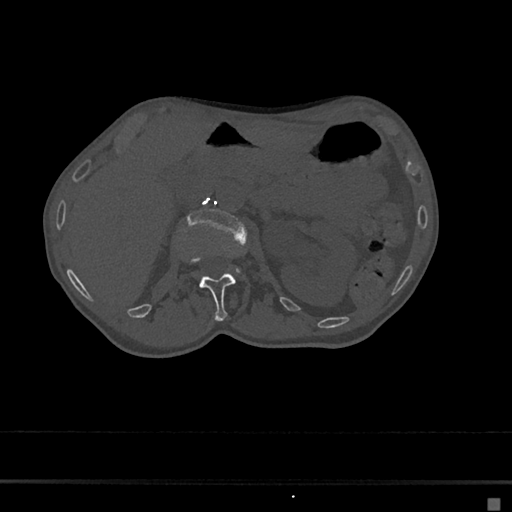
CT including the spine, one axial slice; slice 56 of 797 in the series (ordered by position); 120 kVp; bone window (W 1800 / L 400 HU); 0.5 mm slice thickness; 512 × 512 image matrix, field of view 360 × 360 mm. Female patient, age 68 years. Case-level facts recorded for this patient, not image findings: primary cancer: renal.
Annotated regions visible in this slice (semi-automatic segmentation, software-assisted and operator-edited):
- L1 vertebra: bounding box [x1, y1, x2, y2] px = [180, 255, 247, 320]
- L2 vertebra: [188, 208, 246, 242]